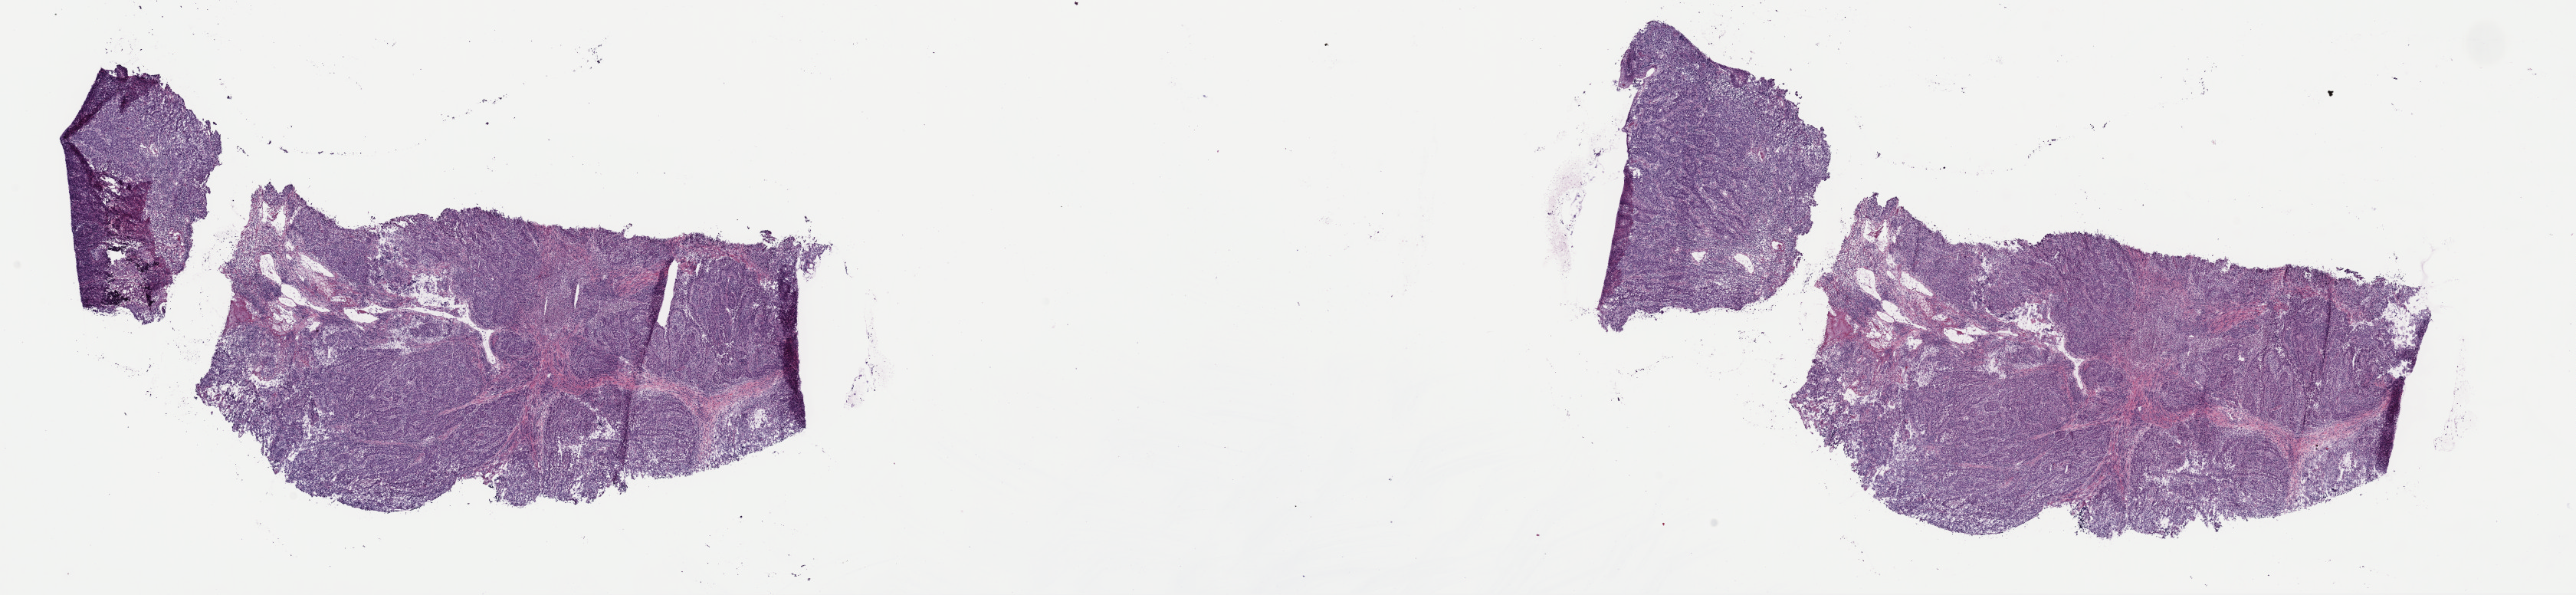
H&E-stained whole-slide image — whole scanned area (about 26.5 x 6.1 mm, slide scanned at 40x) shown as a low-resolution overview. Frozen section from the top of the tissue portion. Esophagus, primary tumour sample. Female, age 79 years at initial diagnosis. Histologic grade: G1 (well differentiated). Slide review estimates, as recorded: tumour cells 60%, tumour nuclei 60%, normal cells 0%, stromal cells 40%, necrosis 0%. Inflammatory infiltration, as recorded: lymphocyte infiltration 25%, monocyte infiltration 0%, neutrophil infiltration 0%.
Lymph nodes positive (case pathology): 0 of 5 examined. Pathologic diagnosis: Adenocarcinoma, NOS. AJCC pathologic stage: I (7th edition).